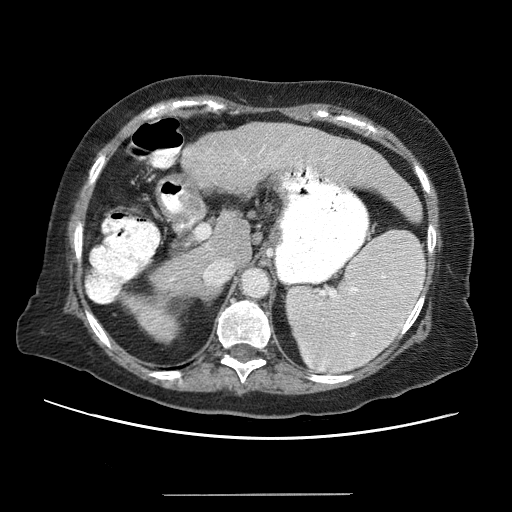
Contrast-enhanced abdominal CT (liver protocol), one axial slice. Slice 36 of 65 in the series (ordered by position). Soft-tissue window (W 400 / L 40 HU). 2.5 mm slice thickness. 512 × 512 image matrix. Case-level facts recorded for this patient, not image findings: diagnosis: hepatocellular carcinoma (patient treated with transarterial chemoembolisation; whether this scan precedes or follows treatment is not stated here); TNM stage (as recorded): Stage-IIIB; Child-Pugh class: A; tumour differentiation: moderately differentiated; tumour nodularity: uninodular.
Structures marked on this image (semi-automatically segmented with operator editing):
- liver parenchyma outside the tumour (the mass and vessels are separate outlines, so this box may not span the whole liver): bounding box (x1, y1, x2, y2) in pixels: (90, 122, 422, 345)
- liver vessels: (96, 138, 371, 332)